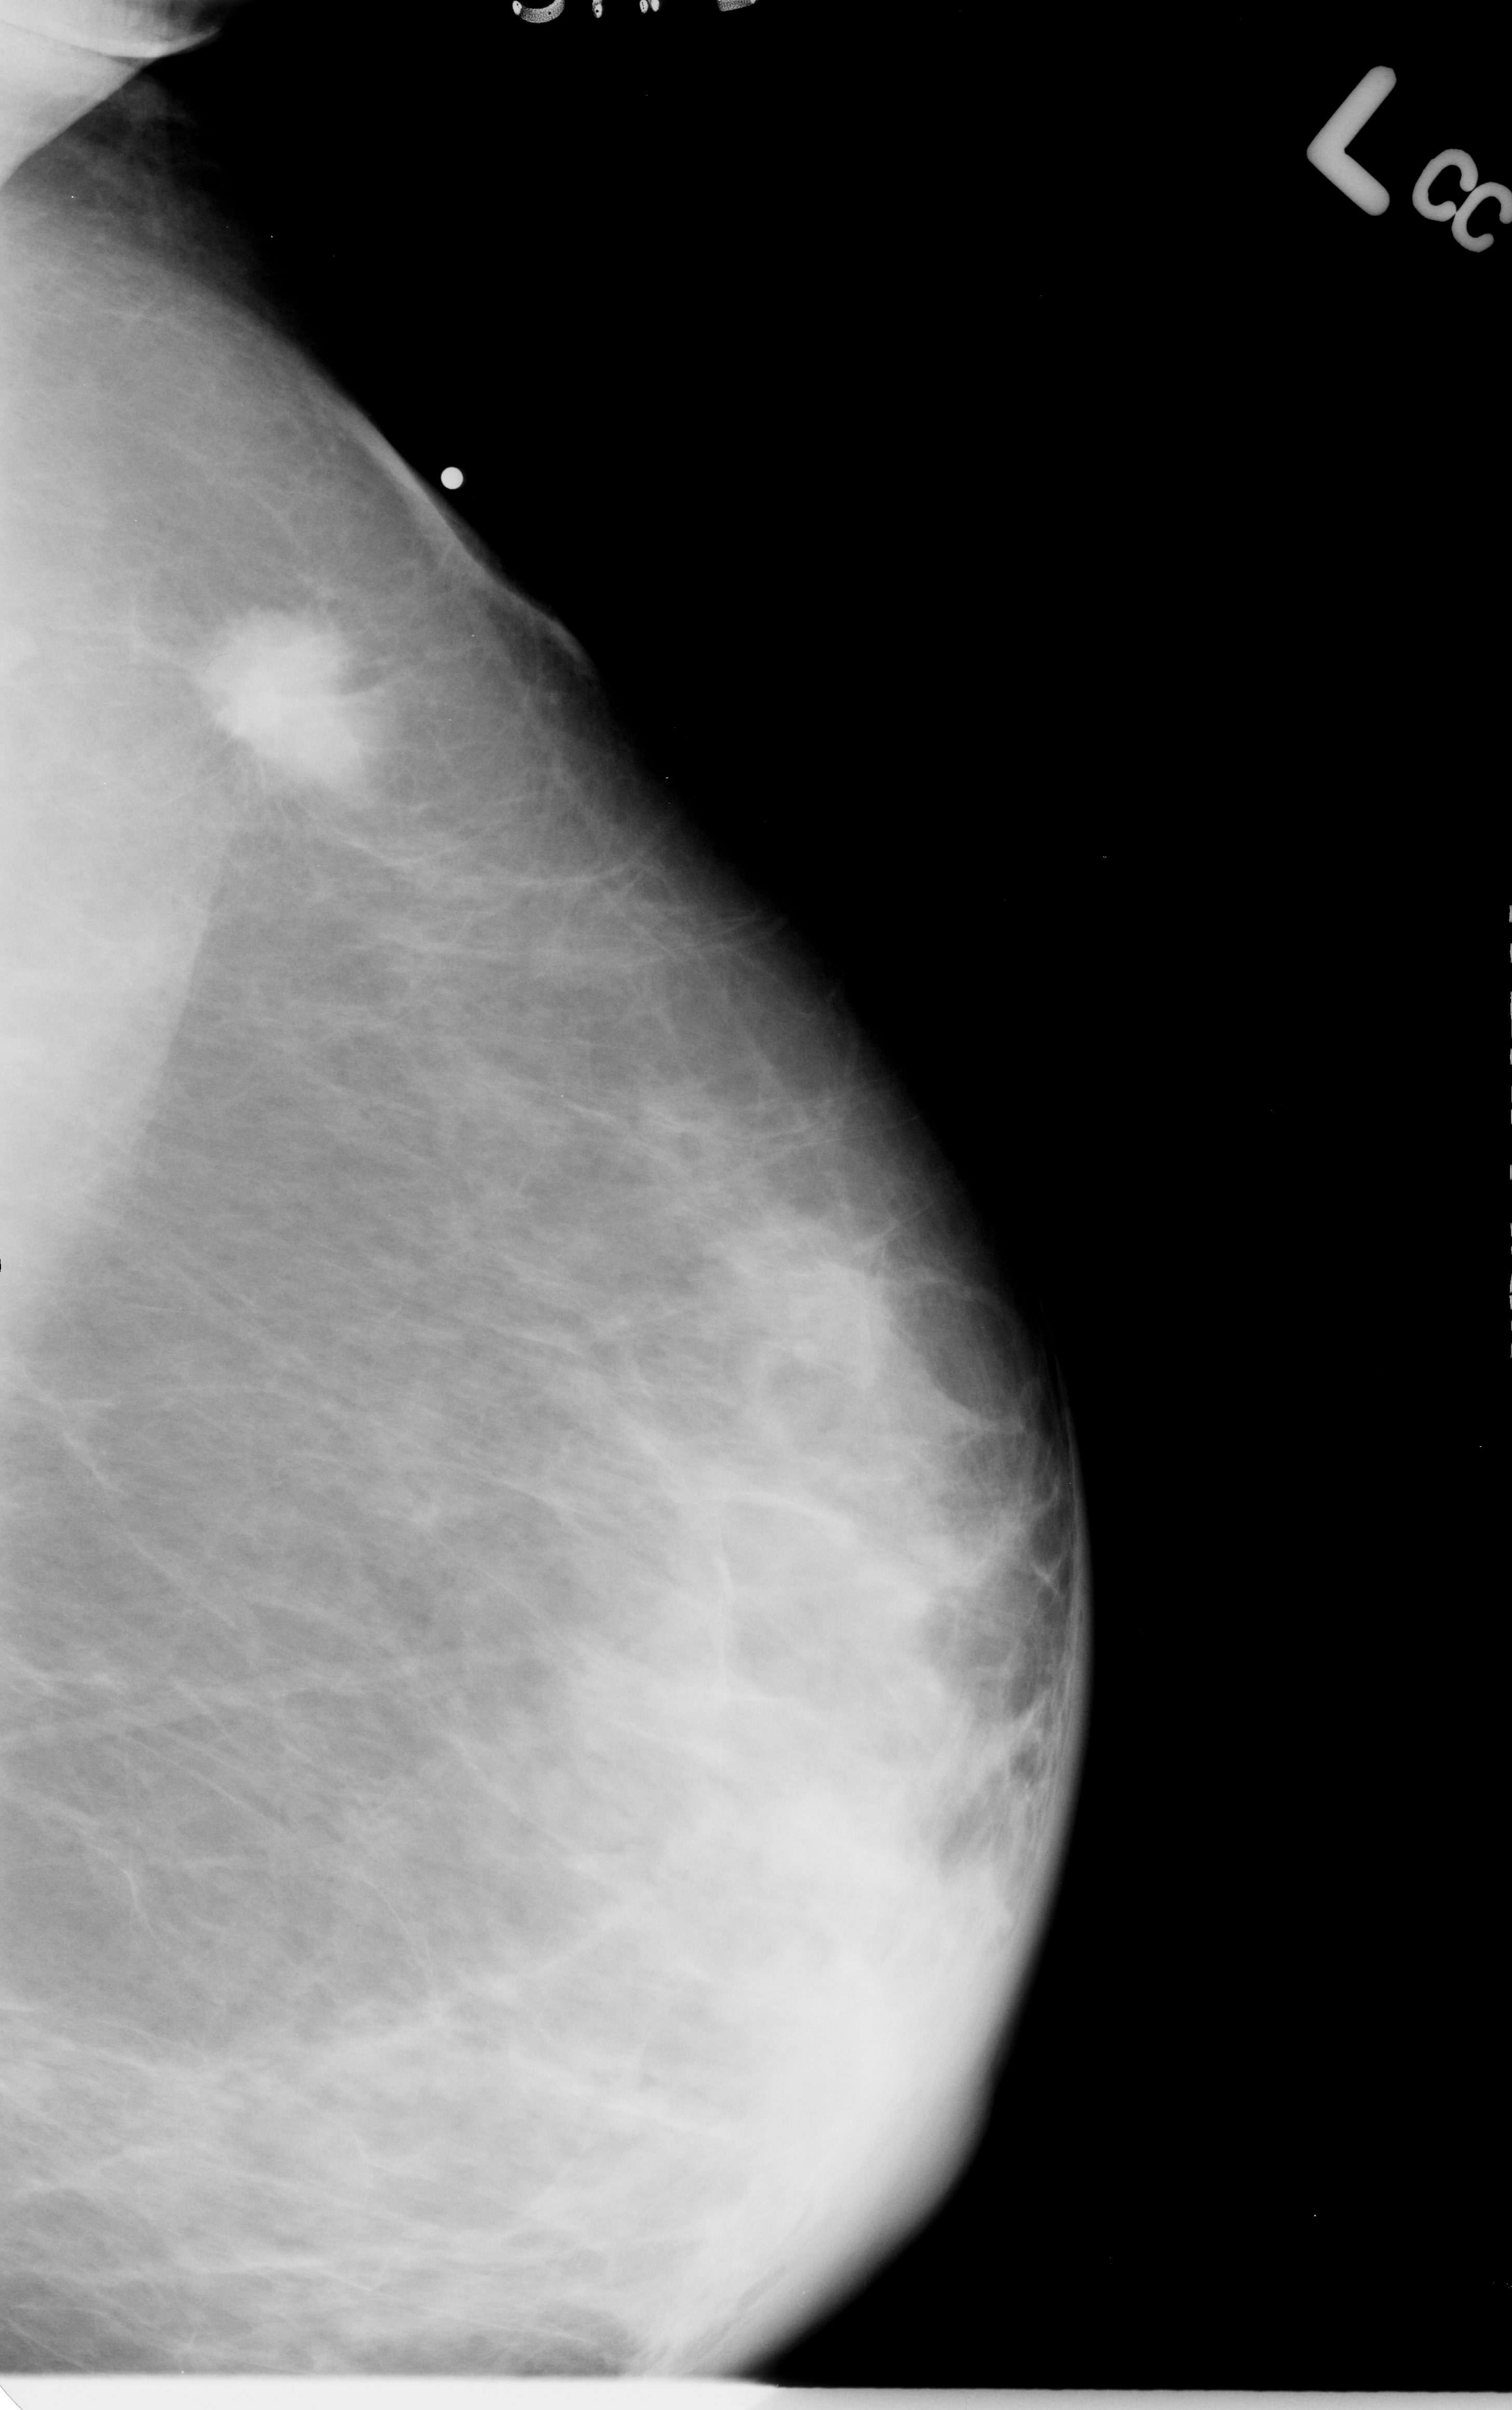
Mammogram (digitized film); left breast; mediolateral oblique (MLO) view; breast composition: heterogeneously dense (BI-RADS density category 3 of 4); 1512 × 2410 image matrix.
Expert-marked regions of interest on this image (one box per marked abnormality):
- mass, shape irregular, margins spiculated; BI-RADS assessment category 5; pathology (as recorded): malignant: bounding box [x1, y1, x2, y2] px = [186, 603, 396, 798]